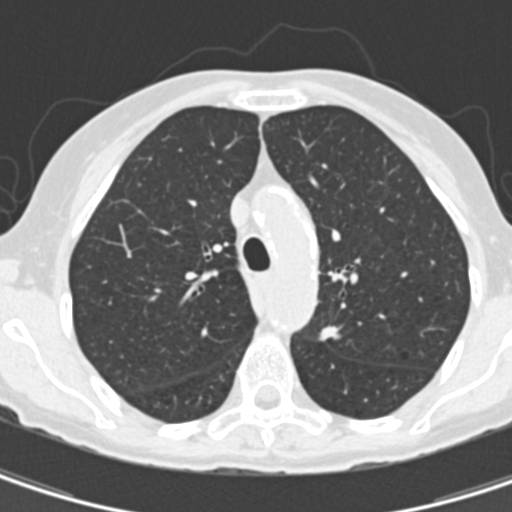
Axial slice from a low-dose chest CT screening exam. Baseline annual screen. Lung window (W 1500 / L -600 HU). Standard (soft-tissue) reconstruction kernel (B30f). Slice 49 of 157 in the series. 512 × 512 image matrix, field of view 260 × 260 mm. Female participant, aged 67 years at enrolment.
Expert reader's lesion annotation, bounding box (x1, y1, x2, y2) in pixels: (313, 315, 356, 363). The exam's reader record, not a measurement of the box and not confirmed to be the same lesion: non-calcified nodule or mass ≥4 mm, left upper lobe, 11 × 8 mm, spiculated (stellate) margins, soft tissue attenuation. Official screen result: positive, change unspecified: nodule(s) >= 4 mm or enlarging nodule(s), mass(es), or other non-specific abnormalities suspicious for lung cancer.